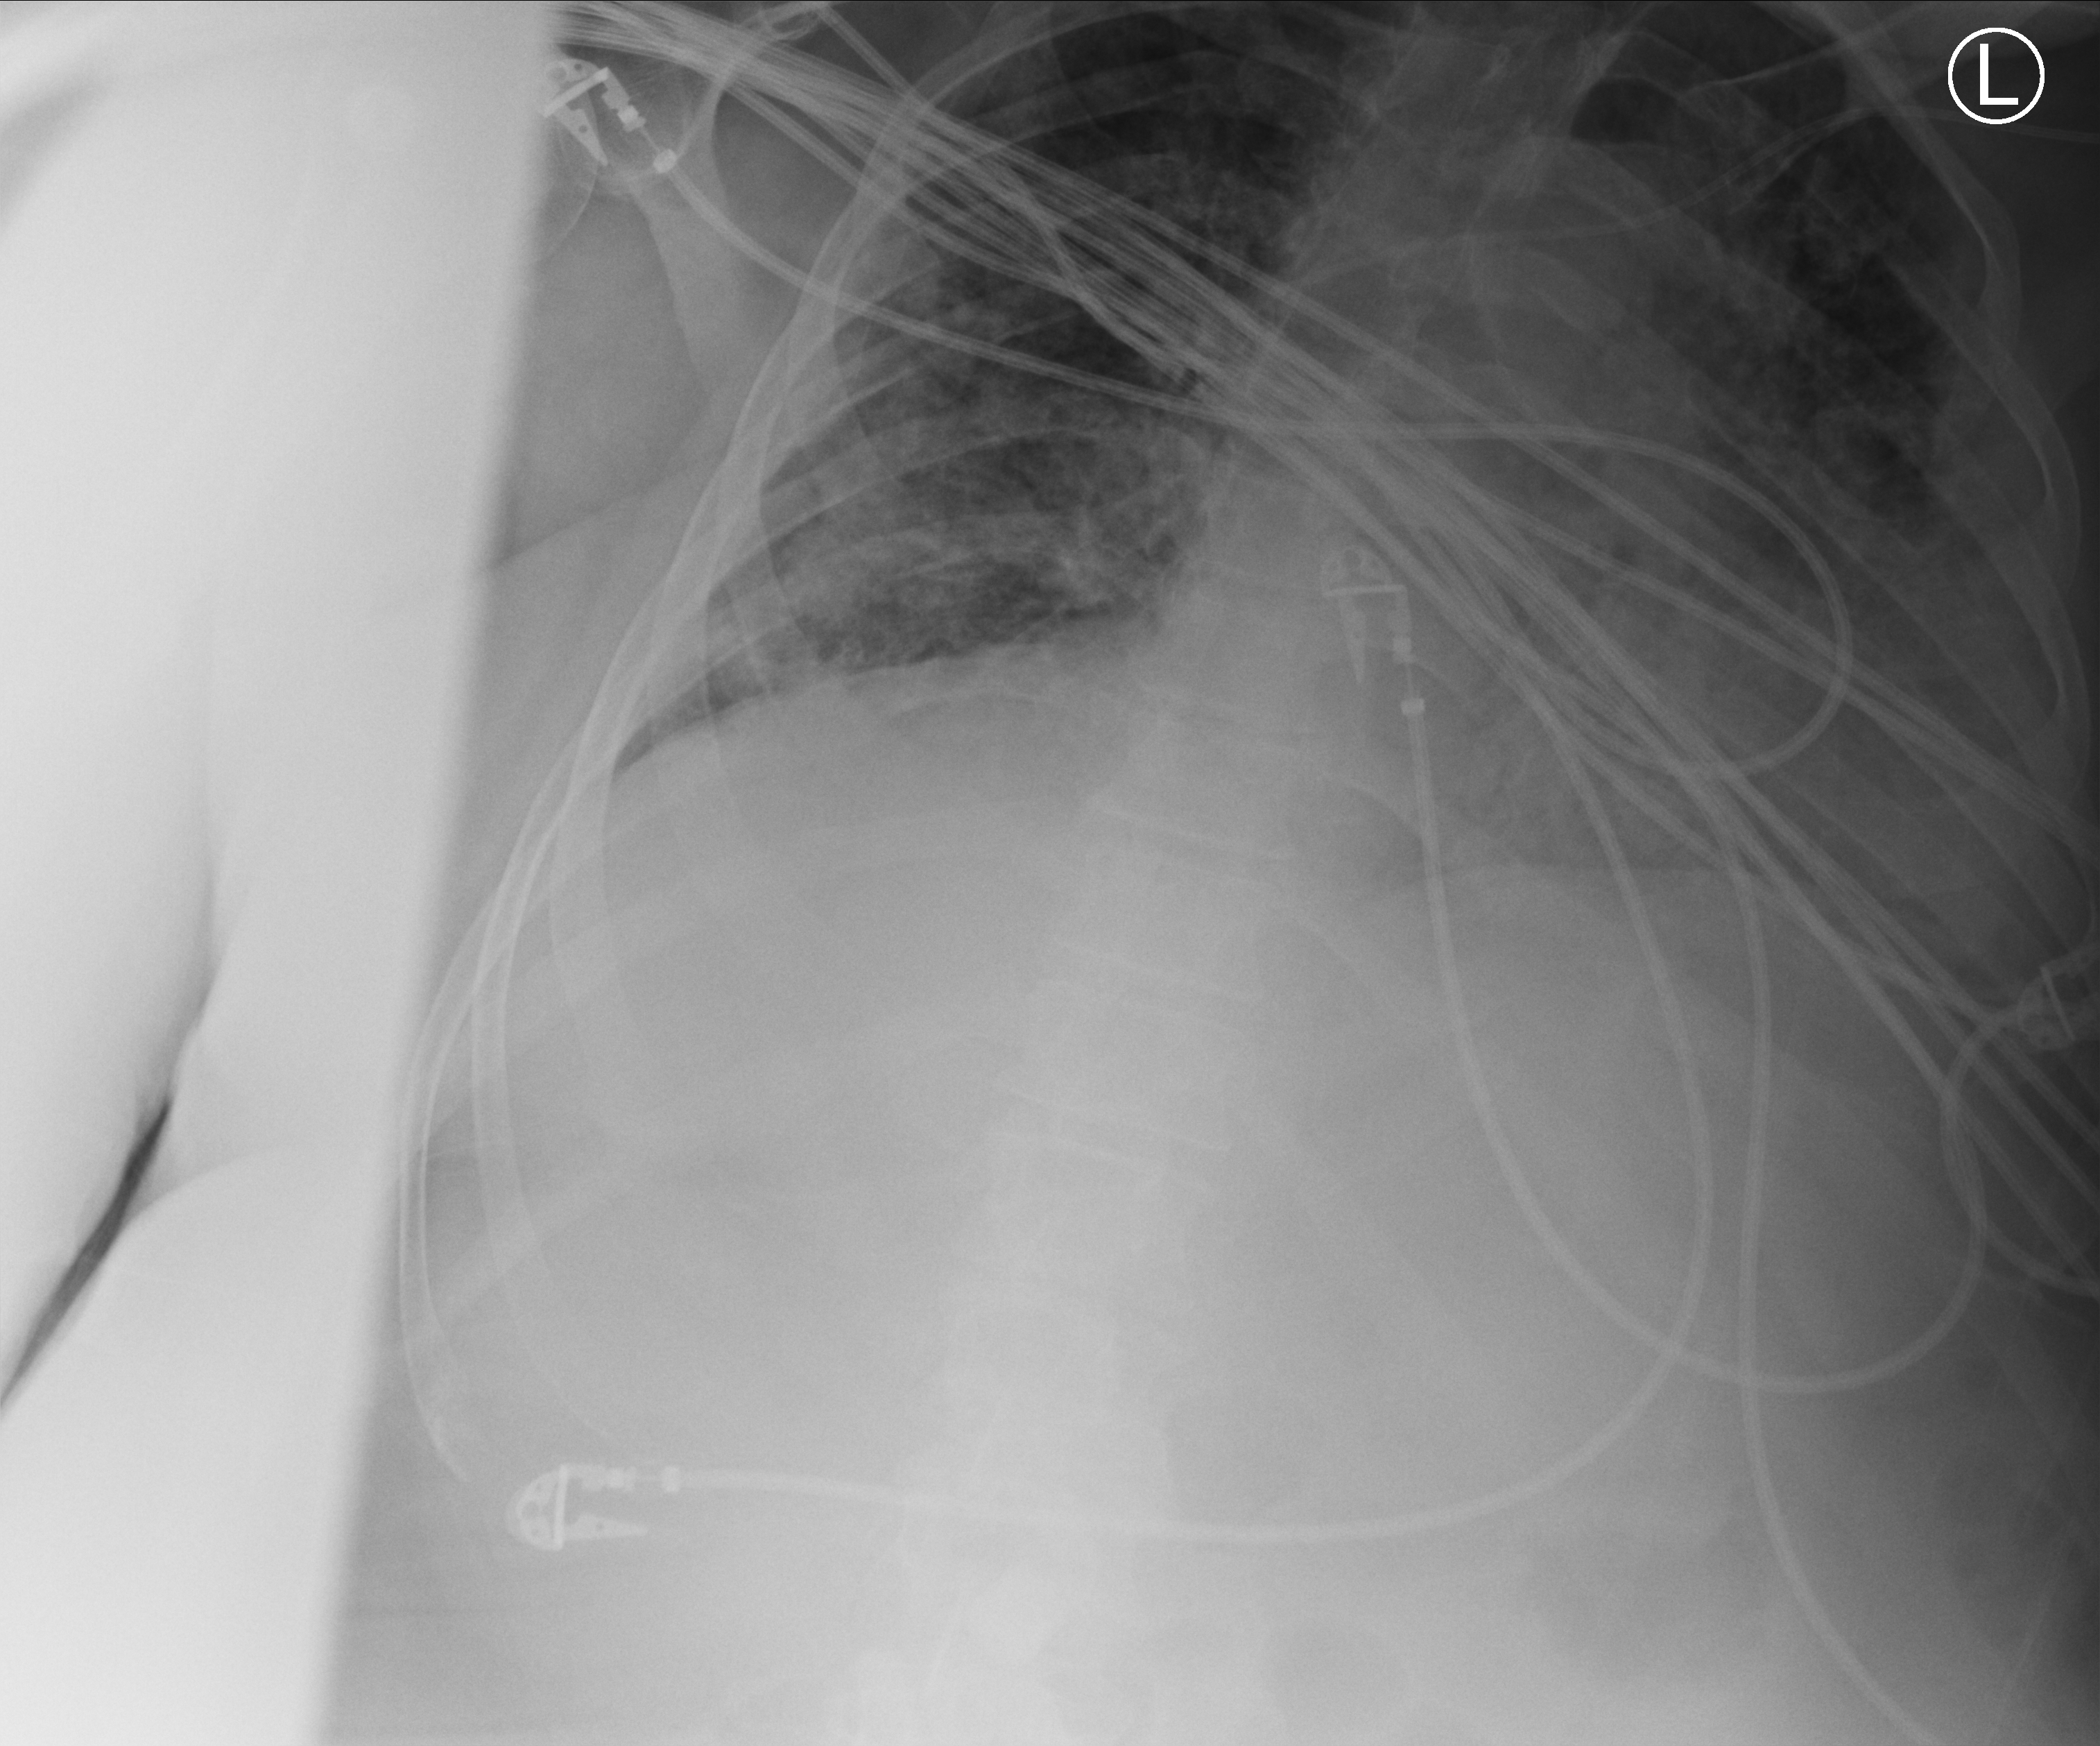
Portable chest radiograph; anteroposterior (AP) projection. Male patient hospitalised with COVID-19, age 18–59 years.
Admission-level facts for this patient (not findings on this image; timing relative to this image not recorded): length of hospital stay: 39 days.